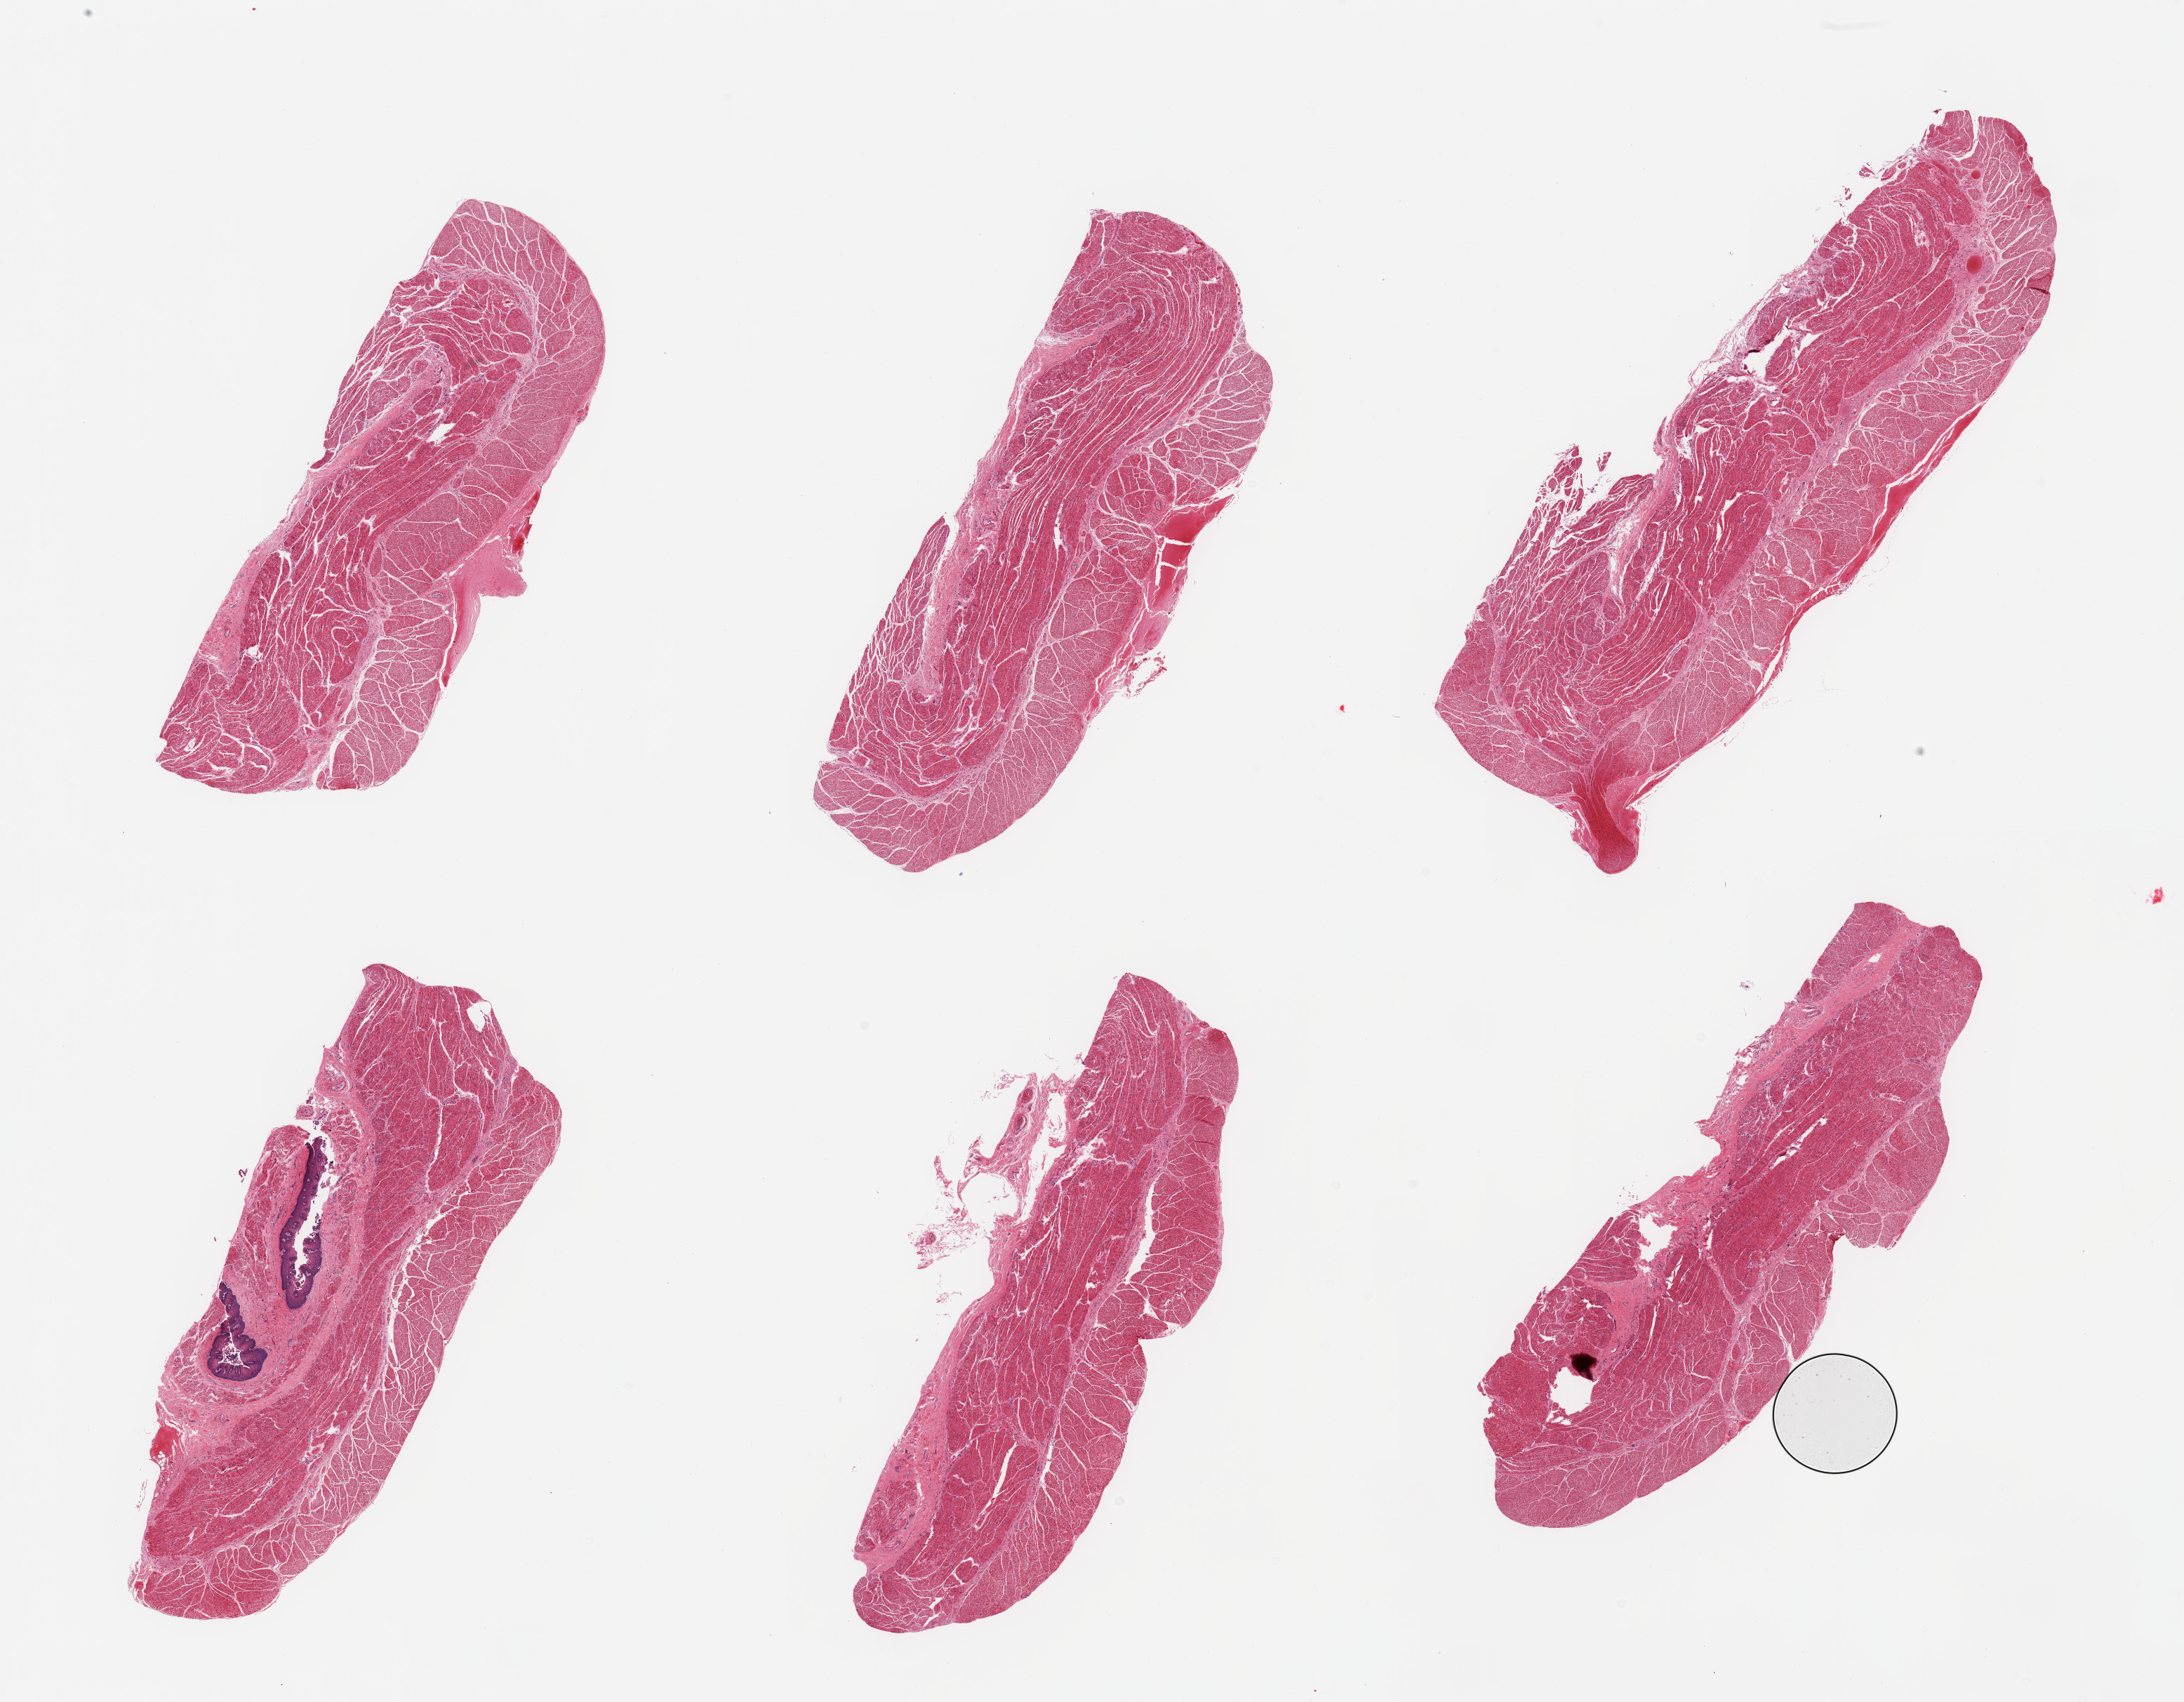
Haematoxylin and eosin whole-slide image, shown as a low-resolution overview of the whole scanned area (about 24.6 x 19.2 mm, from a 20x scan); PAXgene-fixed, paraffin-embedded tissue; section of esophageal muscle (target tissue); tissue donor sample.
Reviewer comment on this tissue sample: 6 pieces, confirmed target muscularis; trace 'contaminant' squamous mucosa.